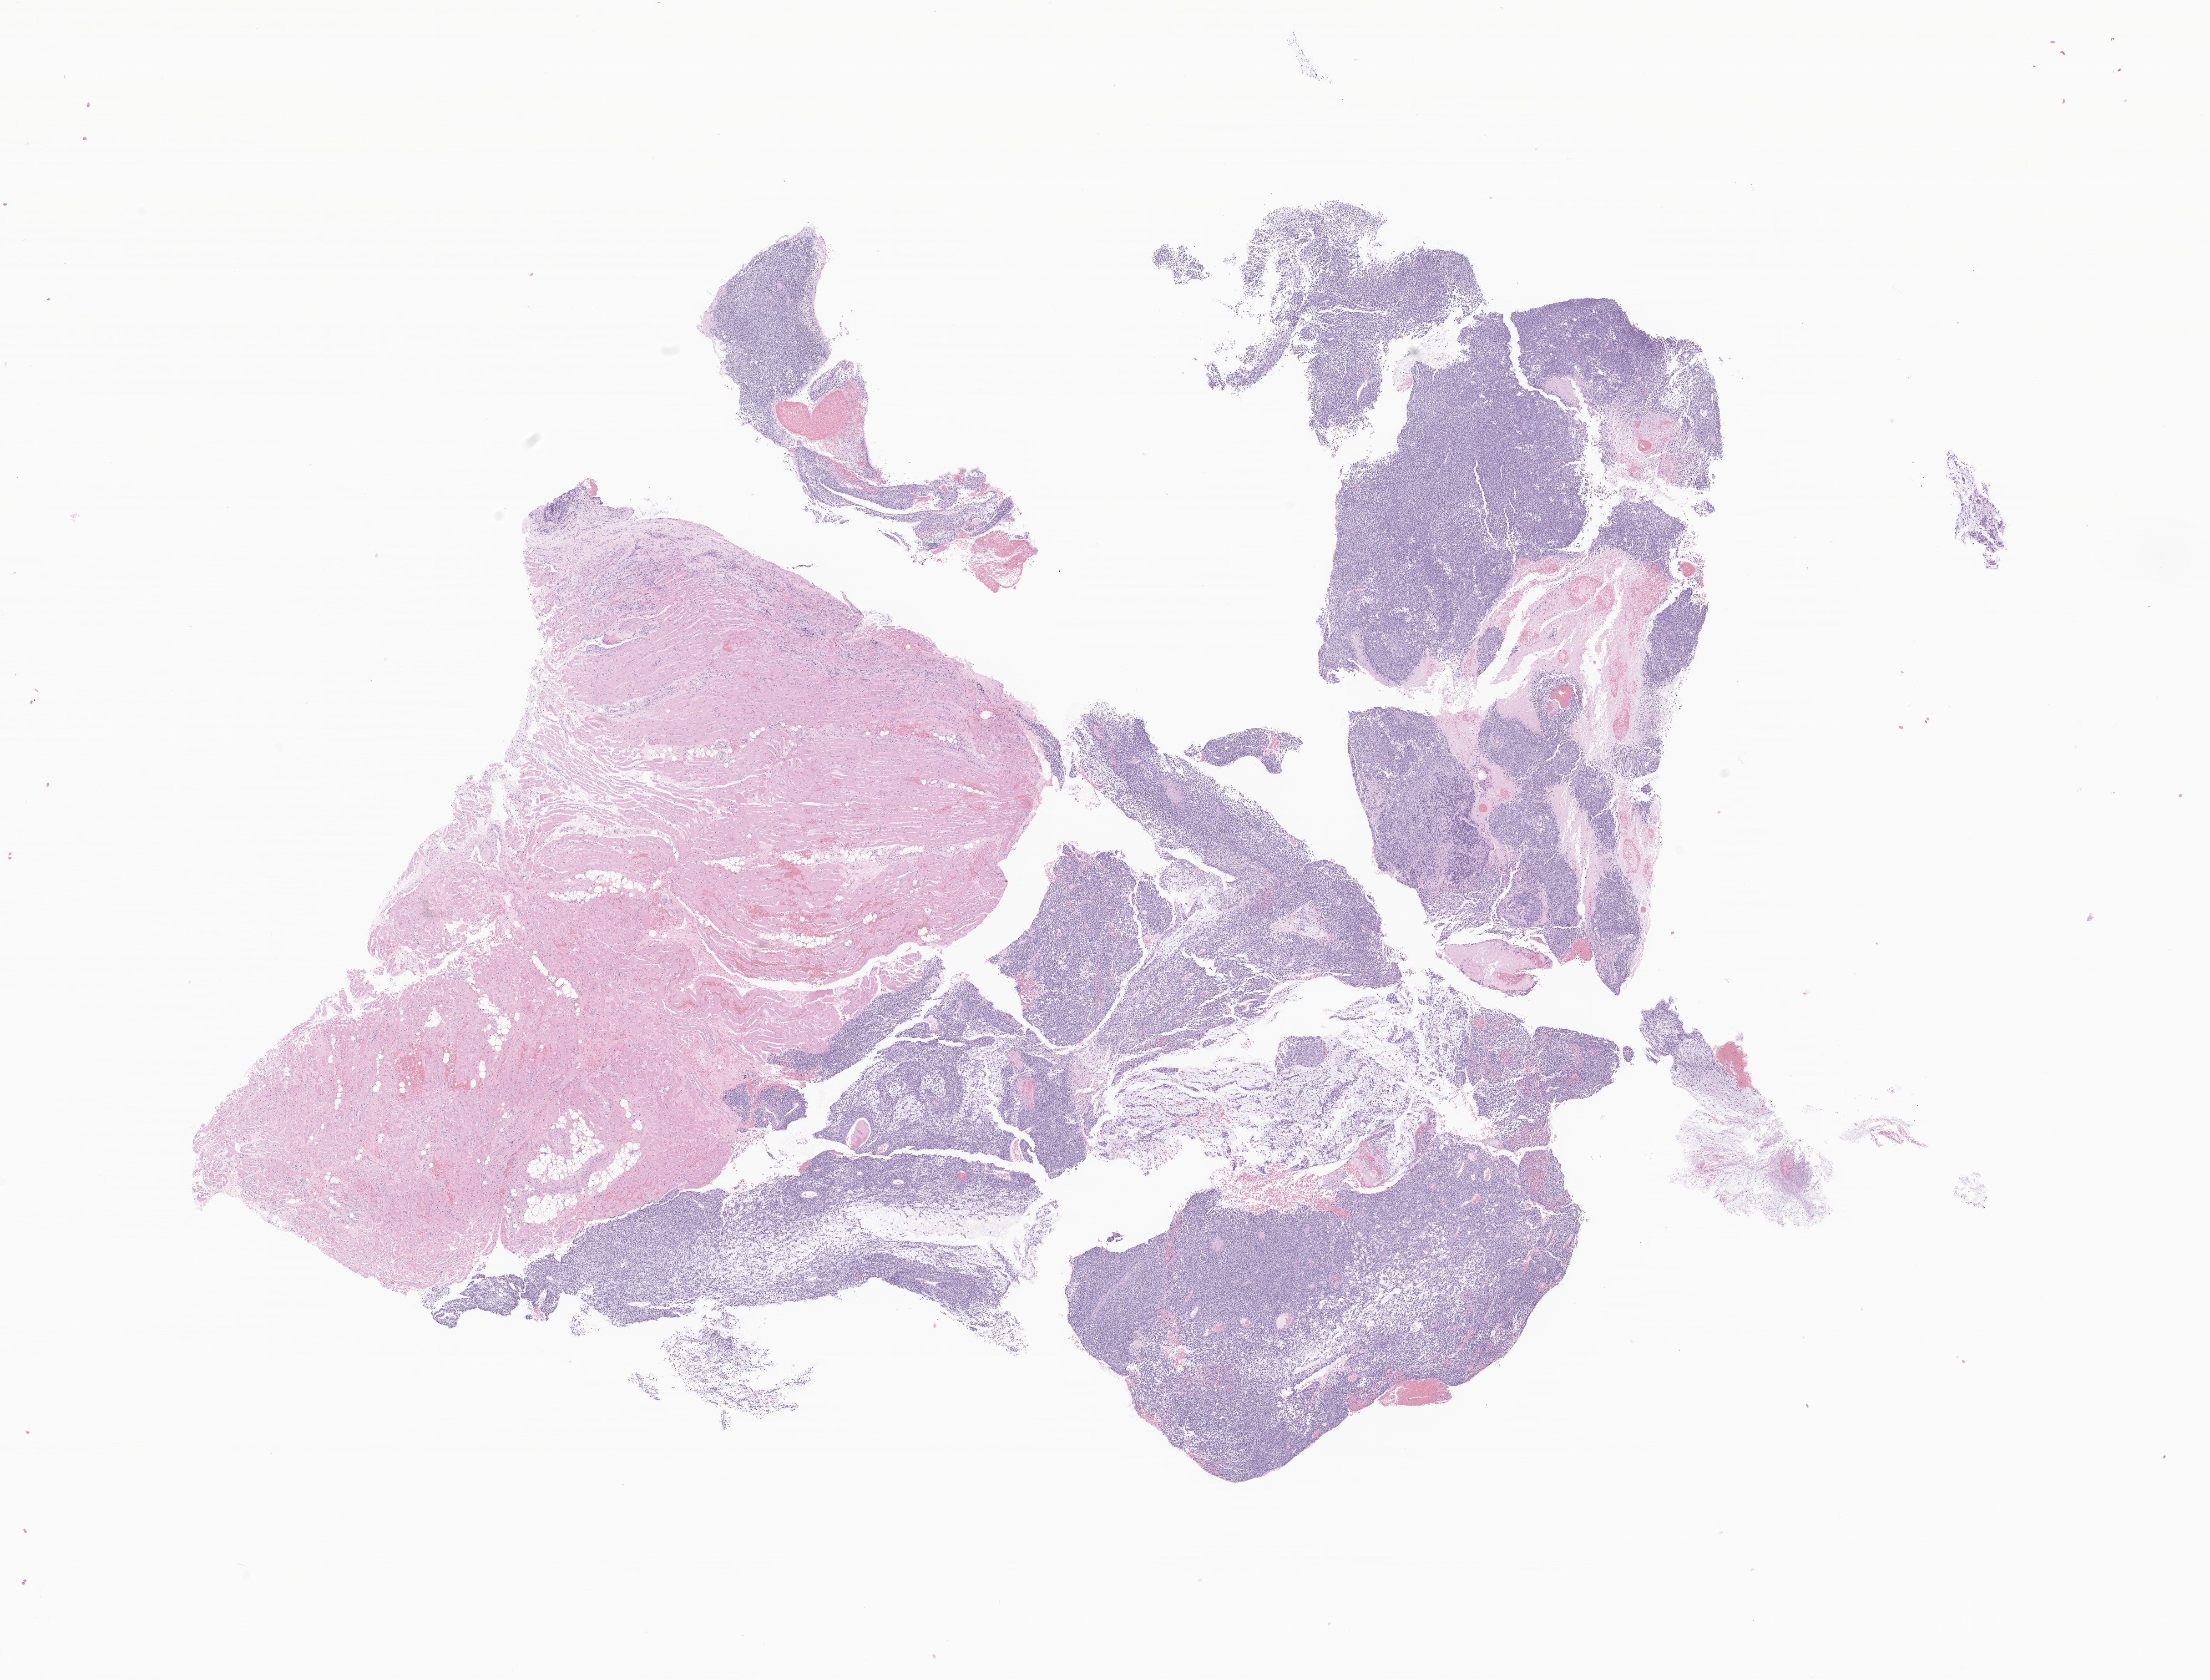
Digitized hematoxylin and eosin (H&E)-stained section of tumor tissue from the head and neck, whole scanned area (about 20.5 x 15.6 mm) shown as a low-resolution overview; FFPE section. Patient: female, age 122 months (10 years 2 months).
• diagnosis: Embryonal rhabdomyosarcoma, NOS
• tissue or organ of origin (case record): head, face or neck